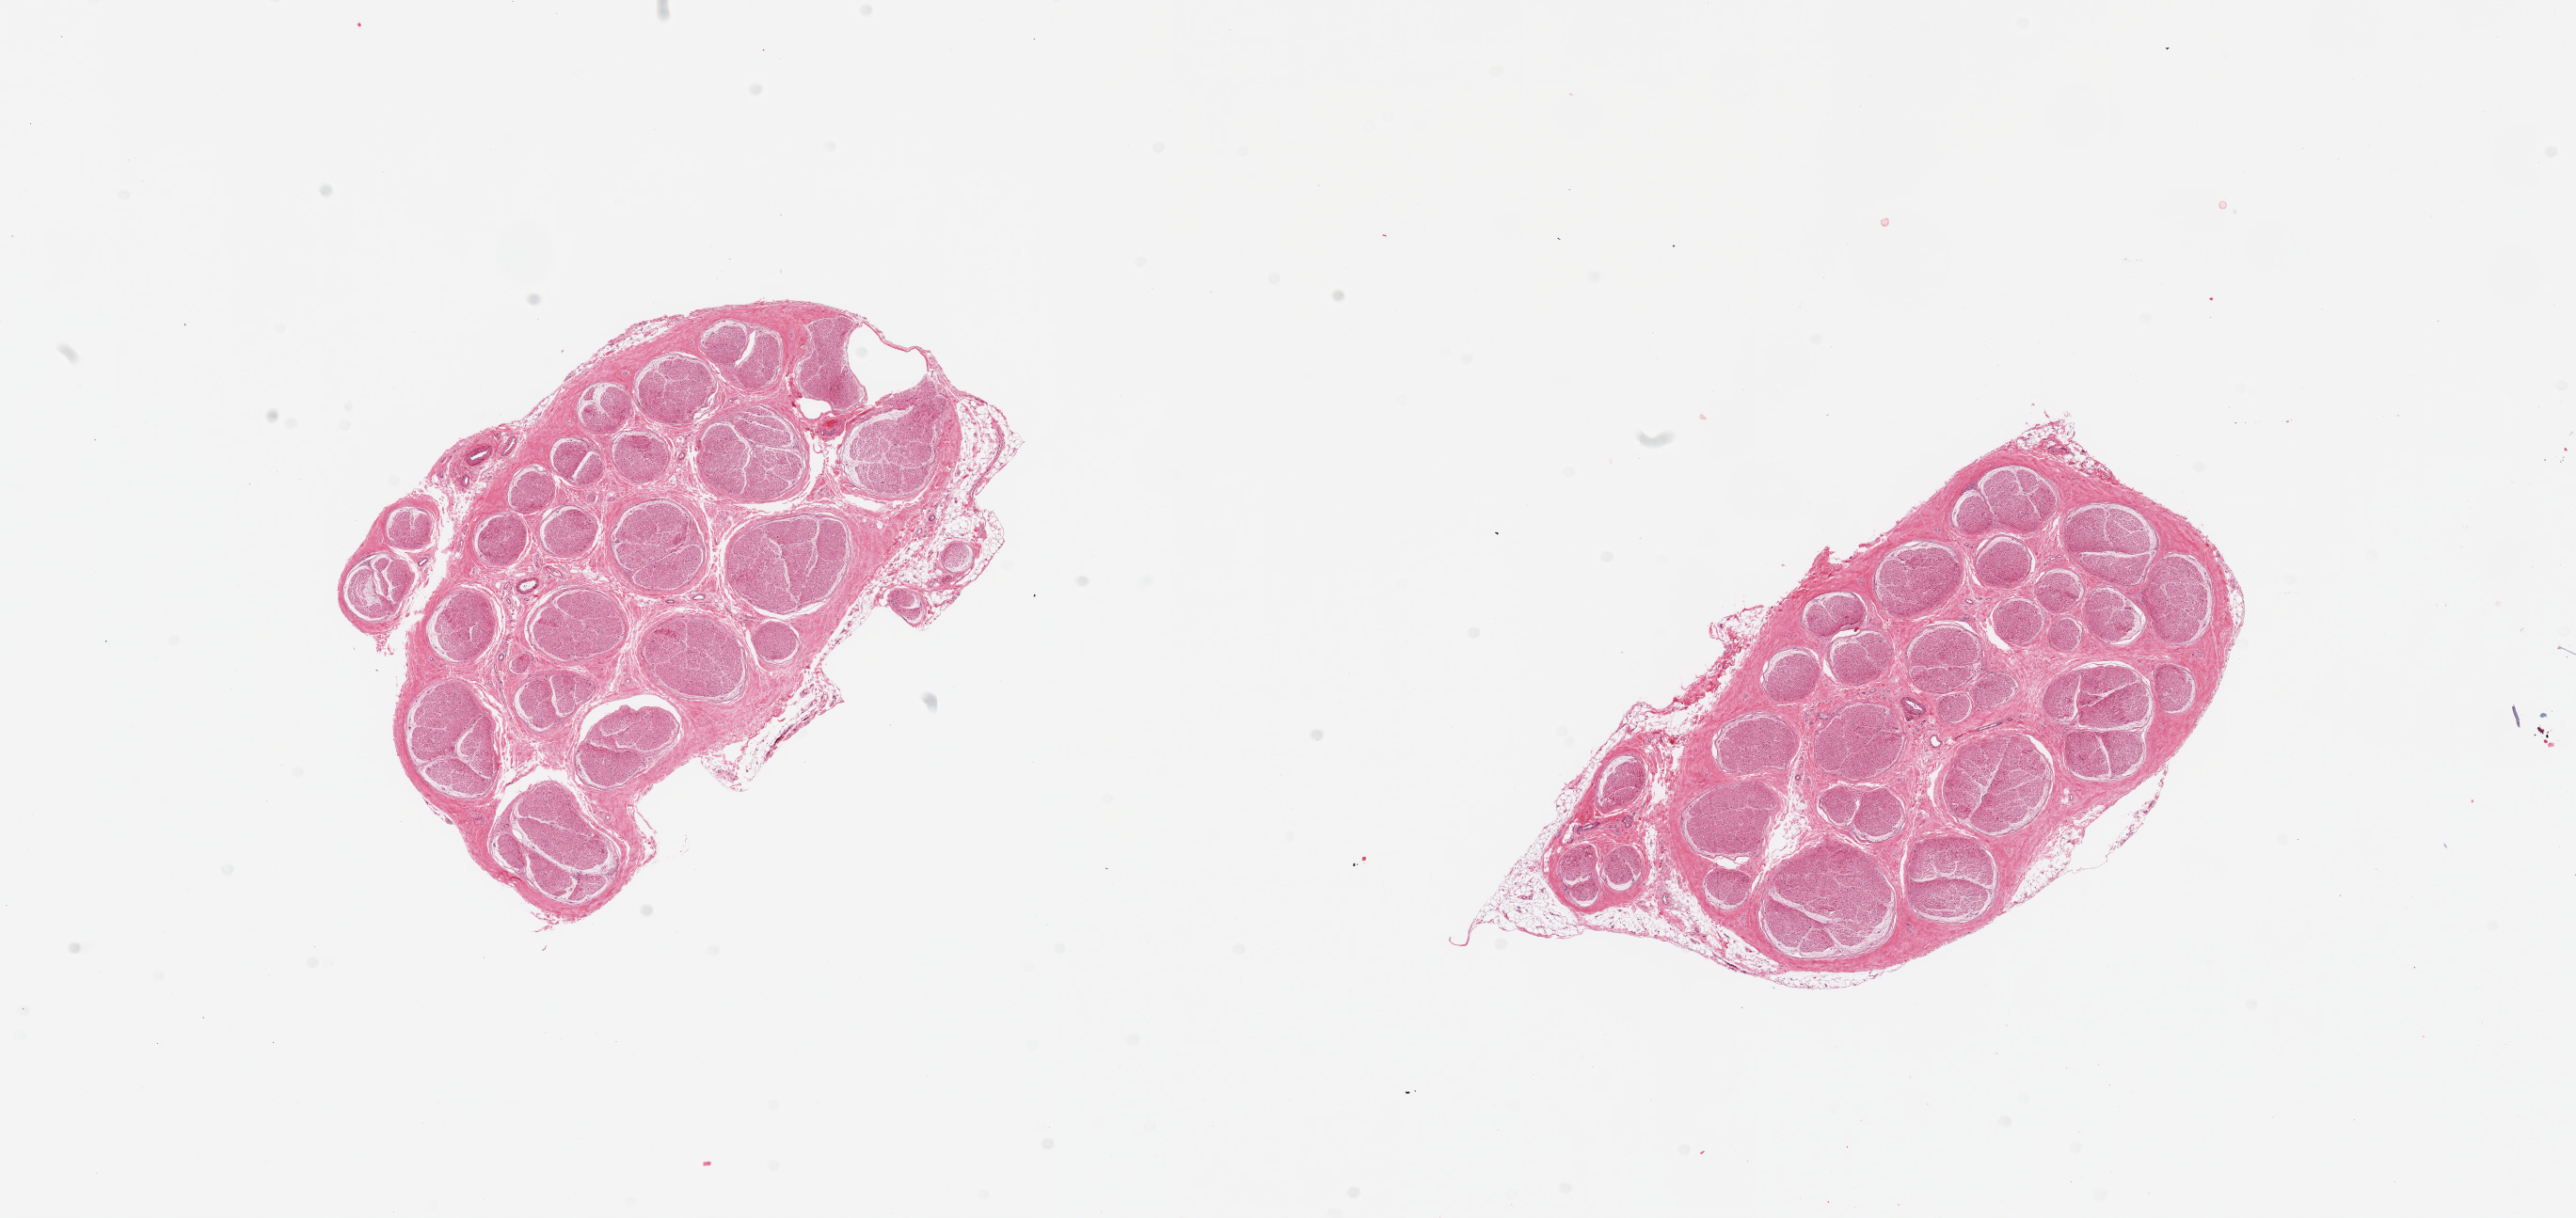
H&E whole-slide image, brightfield — shown as a low-resolution overview of the whole scanned area (about 21.7 x 10.2 mm, slide scanned at 20x), PAXgene-fixed paraffin-embedded (PFPE) section, section of tibial nerve (target tissue), tissue donor sample.
Reviewer comment on this tissue sample: 2 pieces.